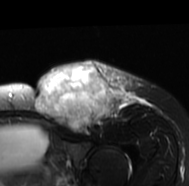
MRI of an extremity soft-tissue mass, one axial slice. Position 51 of 77 along the scan axis. T2-weighted fat-saturated. MR volume resampled by the dataset authors to the PET/CT grid (not the native acquisition matrix). 3.27 mm slice thickness. 189 × 186 image matrix, field of view 185 × 182 mm. Female patient. Case-level facts recorded for this patient, not image findings: histological type: leiomyosarcoma; grade: high; site of the primary tumour: groin.
Annotated regions visible in this slice (expert contour drawn on MRI and transferred to this co-registered scan by the dataset authors):
- gross tumour volume including surrounding oedema: box from (x=33, y=60) to (x=148, y=135) px
- gross tumour volume (mass): (x=33, y=63)–(x=114, y=131)